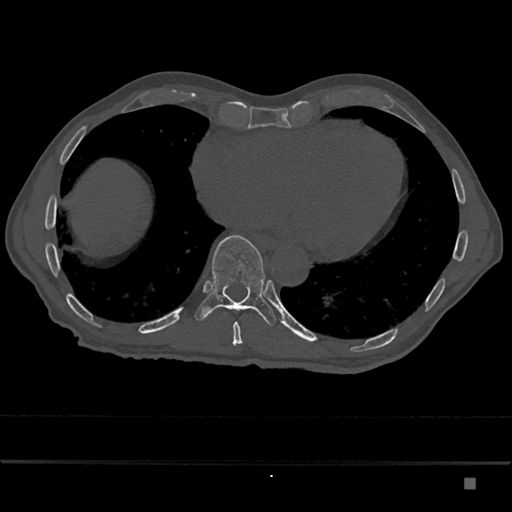
CT including the spine, one axial slice. Slice 756 of 797 in the series (ordered by position). 120 kVp. Bone window (W 1800 / L 400 HU). 512 × 512 image matrix, field of view 390 × 390 mm. Patient: male, 72 years. From the clinical record (not read from this slice): primary cancer: prostate.
Structures marked on this image (semi-automatic segmentation, software-assisted and operator-edited):
- T10 vertebra: bounding box [x1, y1, x2, y2] px = [194, 235, 277, 326]
- T9 vertebra: [232, 322, 243, 346]